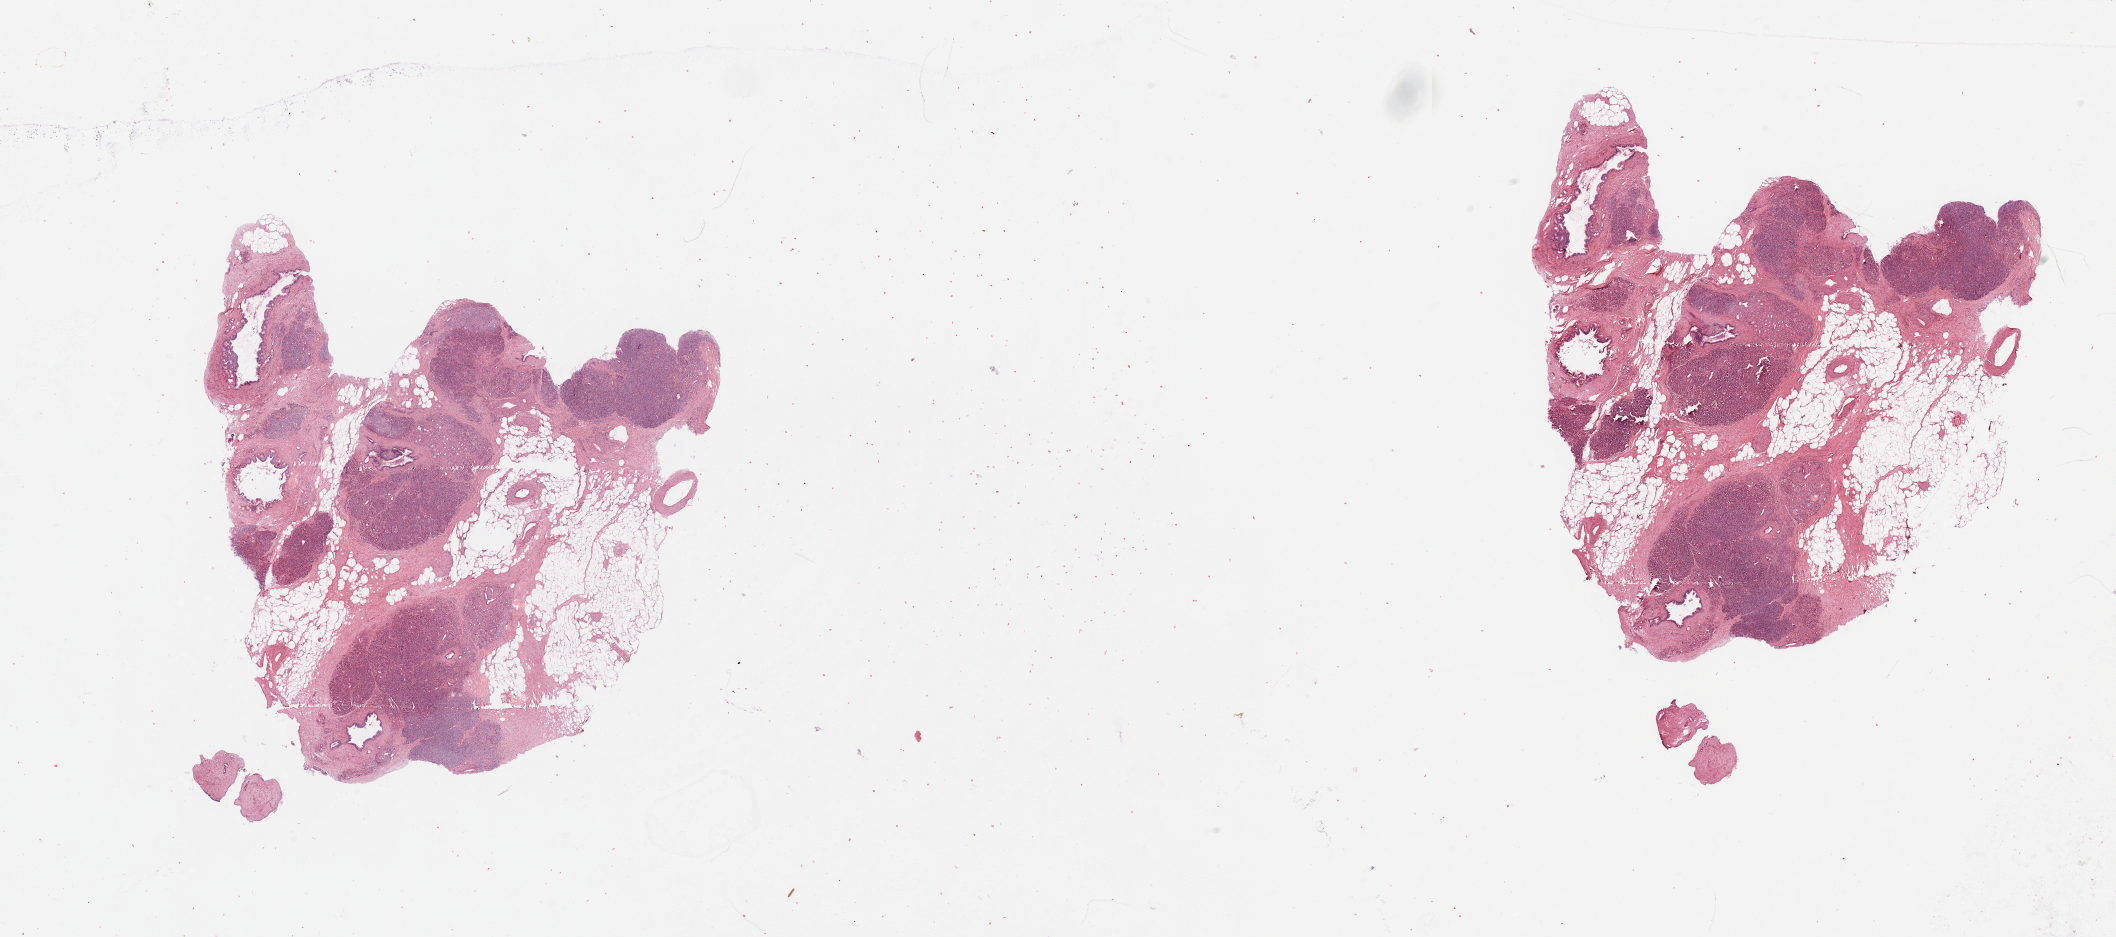
H&E whole-slide image — whole scanned area (about 33.5 x 14.8 mm) shown as a low-resolution overview. Pancreas, tissue type not recorded.
Patient diagnosis (cohort enrolment): ductal adenocarcinoma (pancreas).